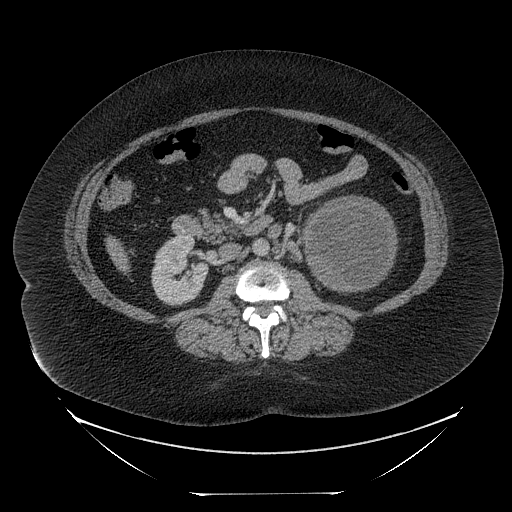
Contrast-enhanced abdominal CT, one axial slice. Position 118 of 205 along the scan axis. 120 kVp. Intravenous contrast given. Soft-tissue window (W 400 / L 40 HU). 2.5 mm slice thickness. 512 × 512 image matrix. Female patient, age 53 years. Case-level facts recorded for this patient, not image findings: diagnosis: adrenocortical carcinoma; tumour side: left adrenal; tumour size at pathology: 17 cm; Ki-67 index: 20 %.
Annotated regions visible in this slice (semi-automatic segmentation, software-assisted and operator-edited):
- mass: bounding box <307,196,396,289> (left, top, right, bottom; pixels)